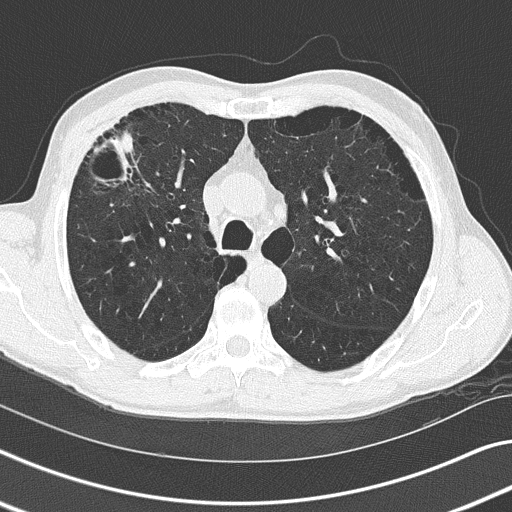
Axial slice from a low-dose chest CT screening exam; third annual screen; lung window (W 1500 / L -600 HU); 2 mm slice thickness; 512 × 512 image matrix. Male, age 66 years at enrolment. Current smoker at enrolment.
• Lesion marked by an expert reader, box from (x=82, y=116) to (x=157, y=201) px.
• The exam's reader record, not a measurement of the box and not confirmed to be the same lesion: non-calcified nodule or mass ≥4 mm, left lower lobe, 9 × 8 mm, smooth margins, soft tissue attenuation, pre-existing on the prior screen: yes; interval growth: no.
• Note: the box lies in the patient's right hemithorax on this image, whereas the reader's record names the left lung; they may be different findings.
• Official screen result: negative screen, significant abnormalities not suspicious for lung cancer.
• Later outcome: lung cancer diagnosed 285 days after this screen — squamous cell carcinoma, adenoid, right upper lobe, poorly differentiated (G3), stage IIB (AJCC 6th edition), 50 mm at pathology.